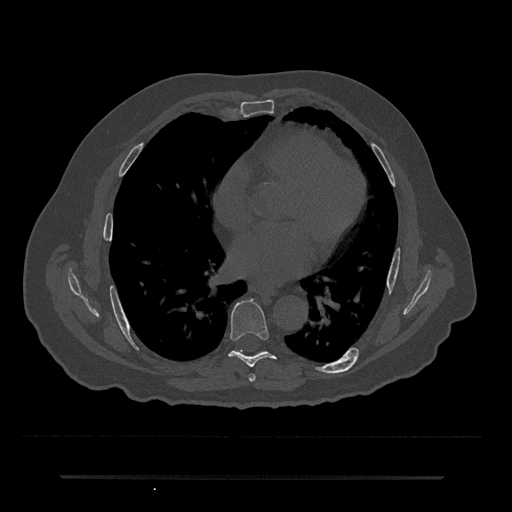
CT including the spine, one axial slice. Slice 379 of 797 in the series (ordered by position). Reconstruction kernel Br40s/3. Bone window (W 1800 / L 400 HU). 512 × 512 image matrix, field of view 437 × 437 mm. Patient: male, 69 years. Case-level facts recorded for this patient, not image findings: primary cancer: prostate.
Outlined on this slice (semi-automatically segmented with operator editing):
- T6 vertebra: bounding box [x1, y1, x2, y2] px = [249, 374, 256, 382]
- T7 vertebra: [229, 299, 276, 367]